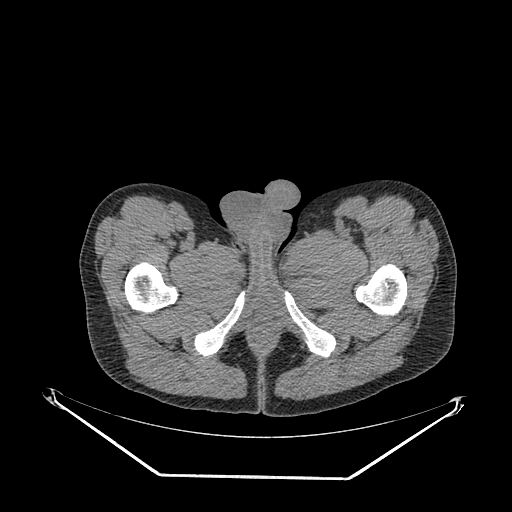
CT of an extremity soft-tissue mass (from a PET/CT study), one axial slice. Slice 46 of 267 in the series (ordered by position). Reconstruction kernel SOFT. 140 kVp. Soft-tissue window (W 400 / L 40 HU). 3.75 mm slice thickness. 512 × 512 image matrix. Male patient. Case-level facts recorded for this patient, not image findings: histological type: pleiomorphic liposarcoma; grade: high; site of the primary tumour: left thigh.
Outlined on this slice (expert contour drawn on MRI and transferred to this co-registered scan by the dataset authors):
- gross tumour volume including surrounding oedema: bounding box (x1, y1, x2, y2) in pixels: (288, 285, 316, 307)